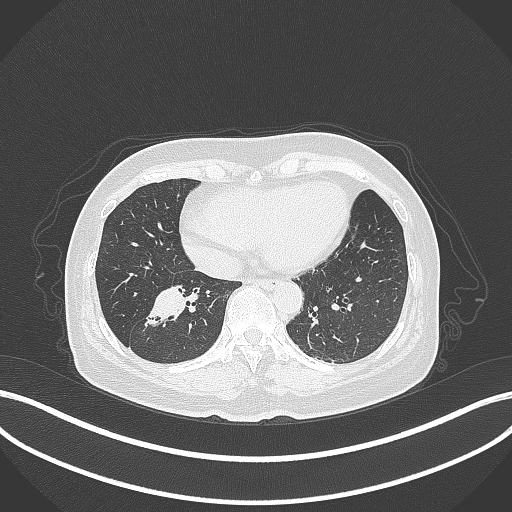
Chest CT, one axial slice. Slice 131 of 429 in the series (ordered by position). Reconstruction kernel B70f. 120 kVp. Lung window (W 1500 / L -600 HU). 1 mm slice thickness. 512 × 512 image matrix. Patient: female, 67 years. From the clinical record (not read from this slice): clinical TNM (as recorded): T1c N1 M0; histopathological grade: G2-3.
Outlined on this slice (bounding box drawn by a radiologist):
- lung tumour (recorded histology: adenocarcinoma): box from (x=142, y=274) to (x=191, y=337) px